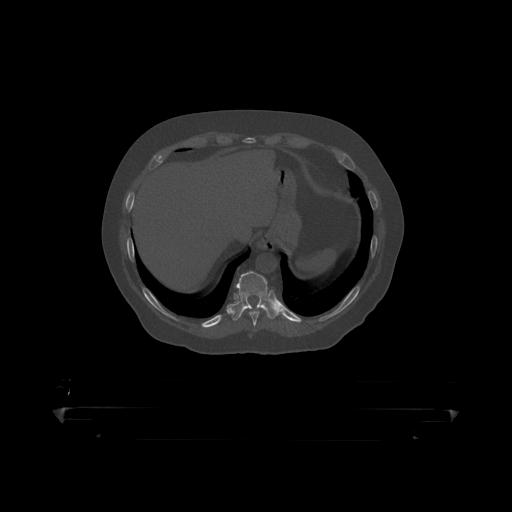
CT including the spine, one axial slice; slice 223 of 390 in the series (ordered by position); bone window (W 1800 / L 400 HU); 1.25 mm slice thickness; 512 × 512 image matrix, field of view 650 × 650 mm. Patient: male, 60 years. From the clinical record (not read from this slice): primary cancer: prostate.
Structures marked on this image (semi-automatic segmentation, software-assisted and operator-edited):
- T10 vertebra: bounding box (x1, y1, x2, y2) in pixels: (233, 272, 279, 318)
- T9 vertebra: (248, 306, 264, 319)